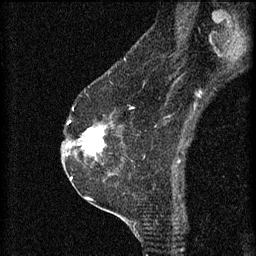
Breast MRI (dynamic contrast-enhanced), one sagittal slice; position 41 of 60 along the scan axis; 3 images stored at this slice position (order not interpretable as contrast timing); 1.5 T; TE 4.2 ms, TR 8.2 ms; 2 mm slice thickness; 256 × 256 image matrix, field of view 180 × 180 mm. Patient: female, 60 years.
Structures marked on this image (semi-automatic segmentation, software-assisted and operator-edited):
- analysis volume of interest (the breast-tissue region the enhancement analysis was run in; not a lesion): bounding box [x1, y1, x2, y2] px = [74, 124, 113, 159]
- tumour enhancement mask (voxels above the 70 % enhancement threshold inside the analysis volume of interest): [74, 128, 105, 155]